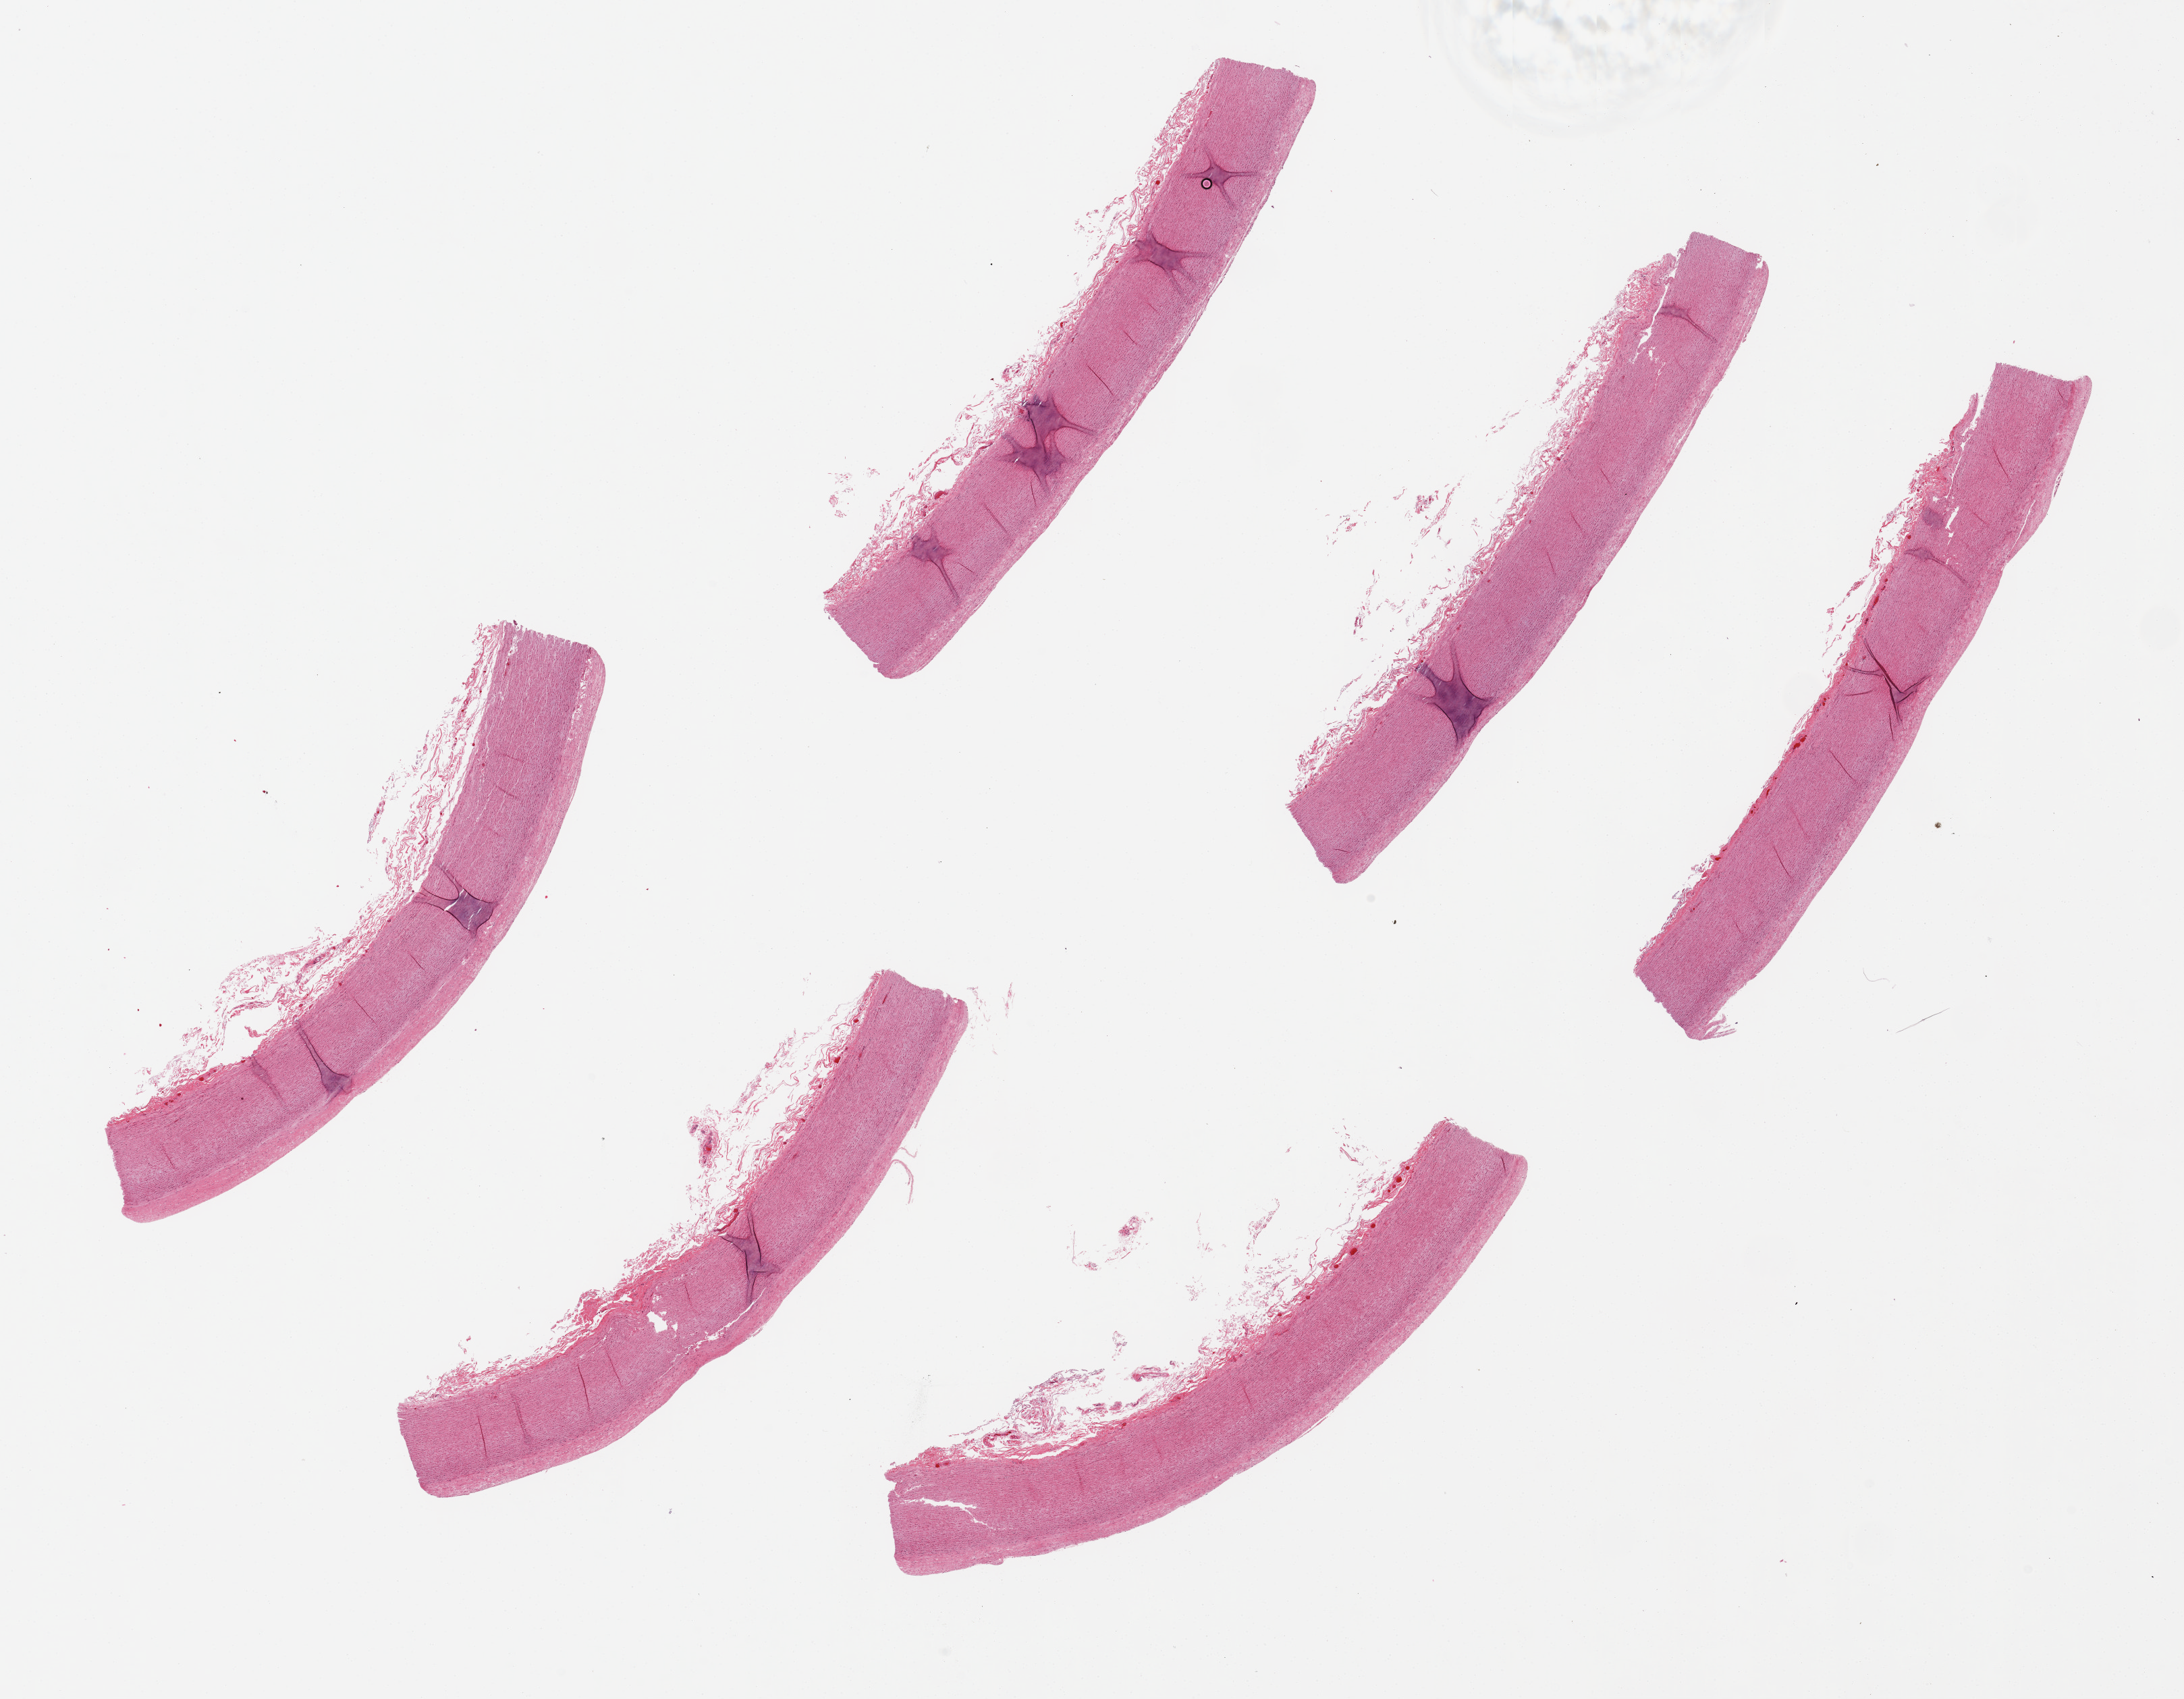
Whole-slide image, H&E stain — low-resolution overview of the scanned area, about 25.6 x 19.9 mm (from a 20x scan), PAXgene-fixed paraffin-embedded (PFPE) section, sampled site (target tissue): aorta, donor tissue sample. Donor: female.
* pathologist's review note for this sample: 6 pieces up to 9x1.3 mm; clean adventitia, minimal plaque